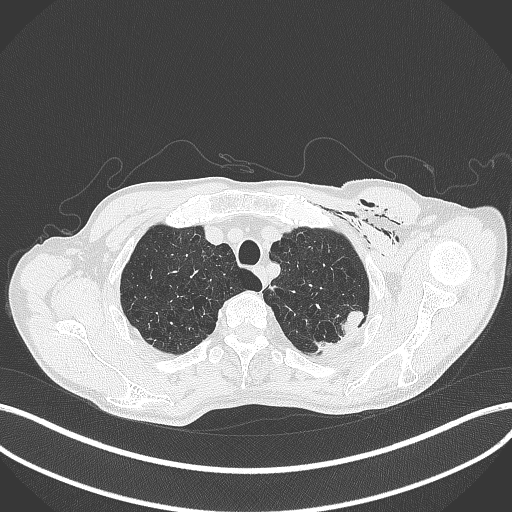
Chest CT, one axial slice. Position 356 of 457 along the scan axis. 120 kVp. Lung window (W 1500 / L -600 HU). 512 × 512 image matrix, field of view 400 × 400 mm. Patient: male, 58 years. From the clinical record (not read from this slice): clinical TNM (as recorded): T3 N0 M0.
Outlined on this slice (rectangle marked by the reading radiologist):
- lung tumour (recorded histology: adenocarcinoma): bounding box (x1, y1, x2, y2) in pixels: (311, 303, 365, 350)